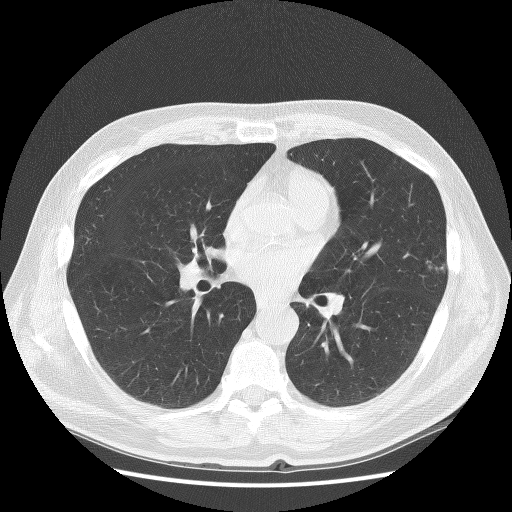
Axial slice from a low-dose chest CT screening exam; baseline screening round; lung window (W 1500 / L -600 HU); 120 kVp; slice 123 of 272 in the series. Male participant, aged 67 years at enrolment. Former smoker at enrolment.
Lesion marked by an expert reader, box from (x=405, y=245) to (x=464, y=294) px. Screening reader's record for this exam: no non-calcified nodule ≥4 mm recorded.